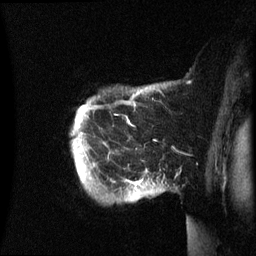
Breast MRI (dynamic contrast-enhanced), one sagittal slice. Dynamic contrast-enhanced series, image 2 of 3 at this slice position (ordered by acquisition). 1.5 T. TE 4.2 ms, TR 8.4 ms. 2.4 mm slice thickness. 256 × 256 image matrix. Female patient, age 49 years.
Annotated regions visible in this slice (semi-automatic segmentation, software-assisted and operator-edited):
- analysis volume of interest (the breast-tissue region the enhancement analysis was run in; not a lesion): bounding box <72,84,166,202> (left, top, right, bottom; pixels)
- tumour enhancement mask (voxels above the 70 % enhancement threshold inside the analysis volume of interest): <135,180,142,185>